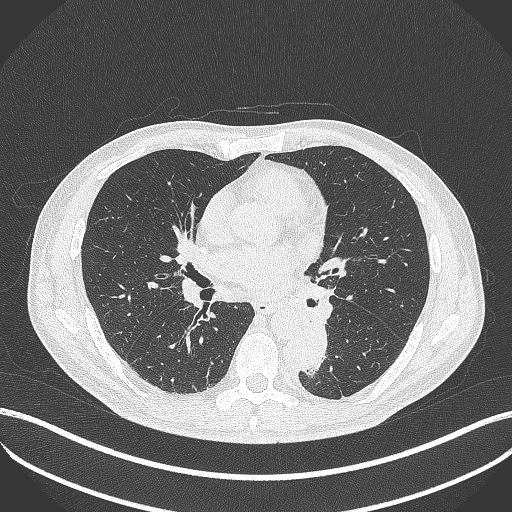
Chest CT, one axial slice. Slice 208 of 451 in the series (ordered by position). Reconstruction kernel B70f. 120 kVp. Lung window (W 1500 / L -600 HU). 512 × 512 image matrix, field of view 400 × 400 mm. Male patient, age 72 years. From the clinical record (not read from this slice): clinical TNM (as recorded): T2b N0 M1.
Outlined on this slice (rectangle marked by the reading radiologist):
- lung tumour (recorded histology: adenocarcinoma): box from (x=281, y=318) to (x=330, y=381) px